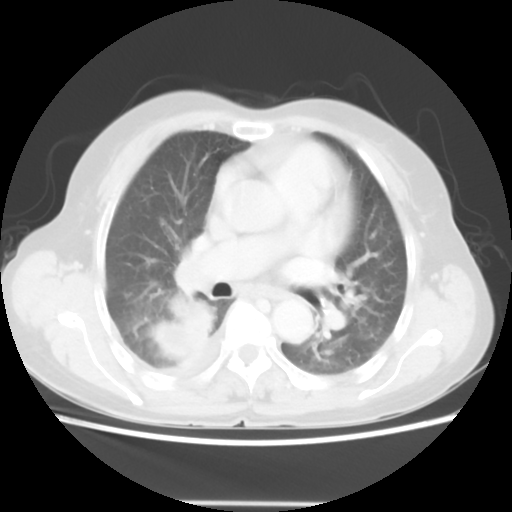
Chest CT, one axial slice; slice 29 of 52 in the series (ordered by position); reconstruction kernel STANDARD; lung window (W 1500 / L -600 HU); 5 mm slice thickness; 512 × 512 image matrix. Female patient, age 67 years. From the clinical record (not read from this slice): clinical TNM (as recorded): T3 N1 M1.
Annotated regions visible in this slice (rectangle marked by the reading radiologist):
- lung tumour (recorded histology: adenocarcinoma): bounding box <150,295,214,365> (left, top, right, bottom; pixels)